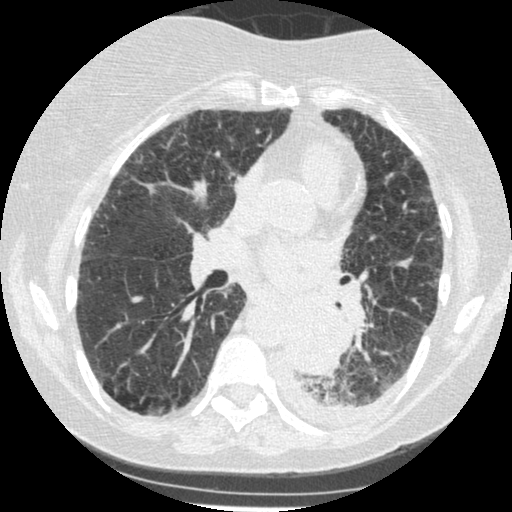
Axial slice from a low-dose chest CT screening exam, third annual screen, lung window (W 1500 / L -600 HU), standard (soft-tissue) reconstruction kernel (STANDARD), slice 214 of 341 in the series, 512 × 512 image matrix. Female, age 60 years at enrolment.
Expert reader's lesion annotation, bounding box [x1, y1, x2, y2] px = [273, 305, 343, 374]. Screening reader's record for this exam (one nodule recorded; not confirmed to be the boxed lesion): non-calcified nodule or mass ≥4 mm, left lower lobe, 54 × 38 mm, smooth margins, soft tissue attenuation, pre-existing on the prior screen: yes; interval growth: yes. Official screen result: positive, other. Participant outcome: lung cancer diagnosed 15 days after this screen — small cell carcinoma, NOS, left lower lobe, undifferentiated (G4), stage IV (AJCC 6th edition), 69 mm at pathology.